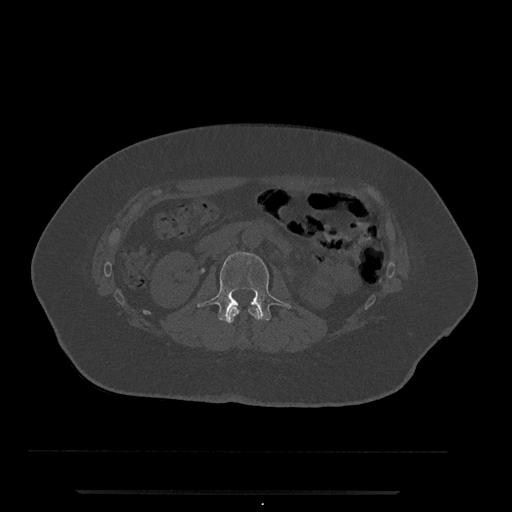
CT including the spine, one axial slice; slice 50 of 797 in the series (ordered by position); reconstruction kernel Br40s/3; bone window (W 1800 / L 400 HU); 0.5 mm slice thickness; 512 × 512 image matrix. Female patient, age 51 years. Case-level facts recorded for this patient, not image findings: primary cancer: neuro.
Structures marked on this image (semi-automatic segmentation, software-assisted and operator-edited):
- L1 vertebra: box from (x=225, y=306) to (x=261, y=324) px
- L2 vertebra: (x=197, y=251)–(x=291, y=322)